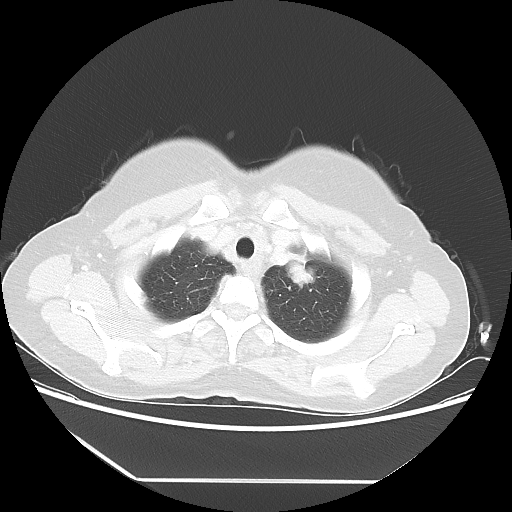
Chest CT, one axial slice; position 46 of 52 along the scan axis; reconstruction kernel LUNG; 100 kVp; lung window (W 1500 / L -600 HU); 5 mm slice thickness; 512 × 512 image matrix, field of view 390 × 390 mm. Female patient, age 50 years. From the clinical record (not read from this slice): clinical TNM (as recorded): T2 N3 M0.
Structures marked on this image (rectangle marked by the reading radiologist):
- lung tumour (recorded histology: adenocarcinoma): bounding box [x1, y1, x2, y2] px = [276, 252, 322, 298]